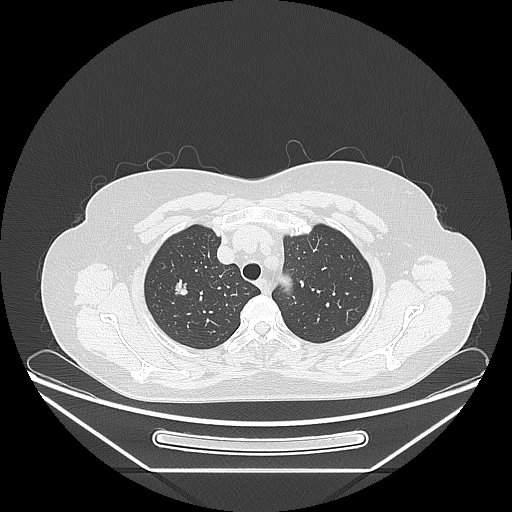
Chest CT, one axial slice; 120 kVp; lung window (W 1500 / L -600 HU); 1.25 mm slice thickness; 512 × 512 image matrix, field of view 433 × 433 mm. Patient: female, 60 years. From the clinical record (not read from this slice): clinical TNM (as recorded): T1c N0 M0; histopathological grade: G2-3.
Structures marked on this image (rectangle marked by the reading radiologist):
- lung tumour (recorded histology: adenocarcinoma): bounding box (x1, y1, x2, y2) in pixels: (170, 275, 193, 303)